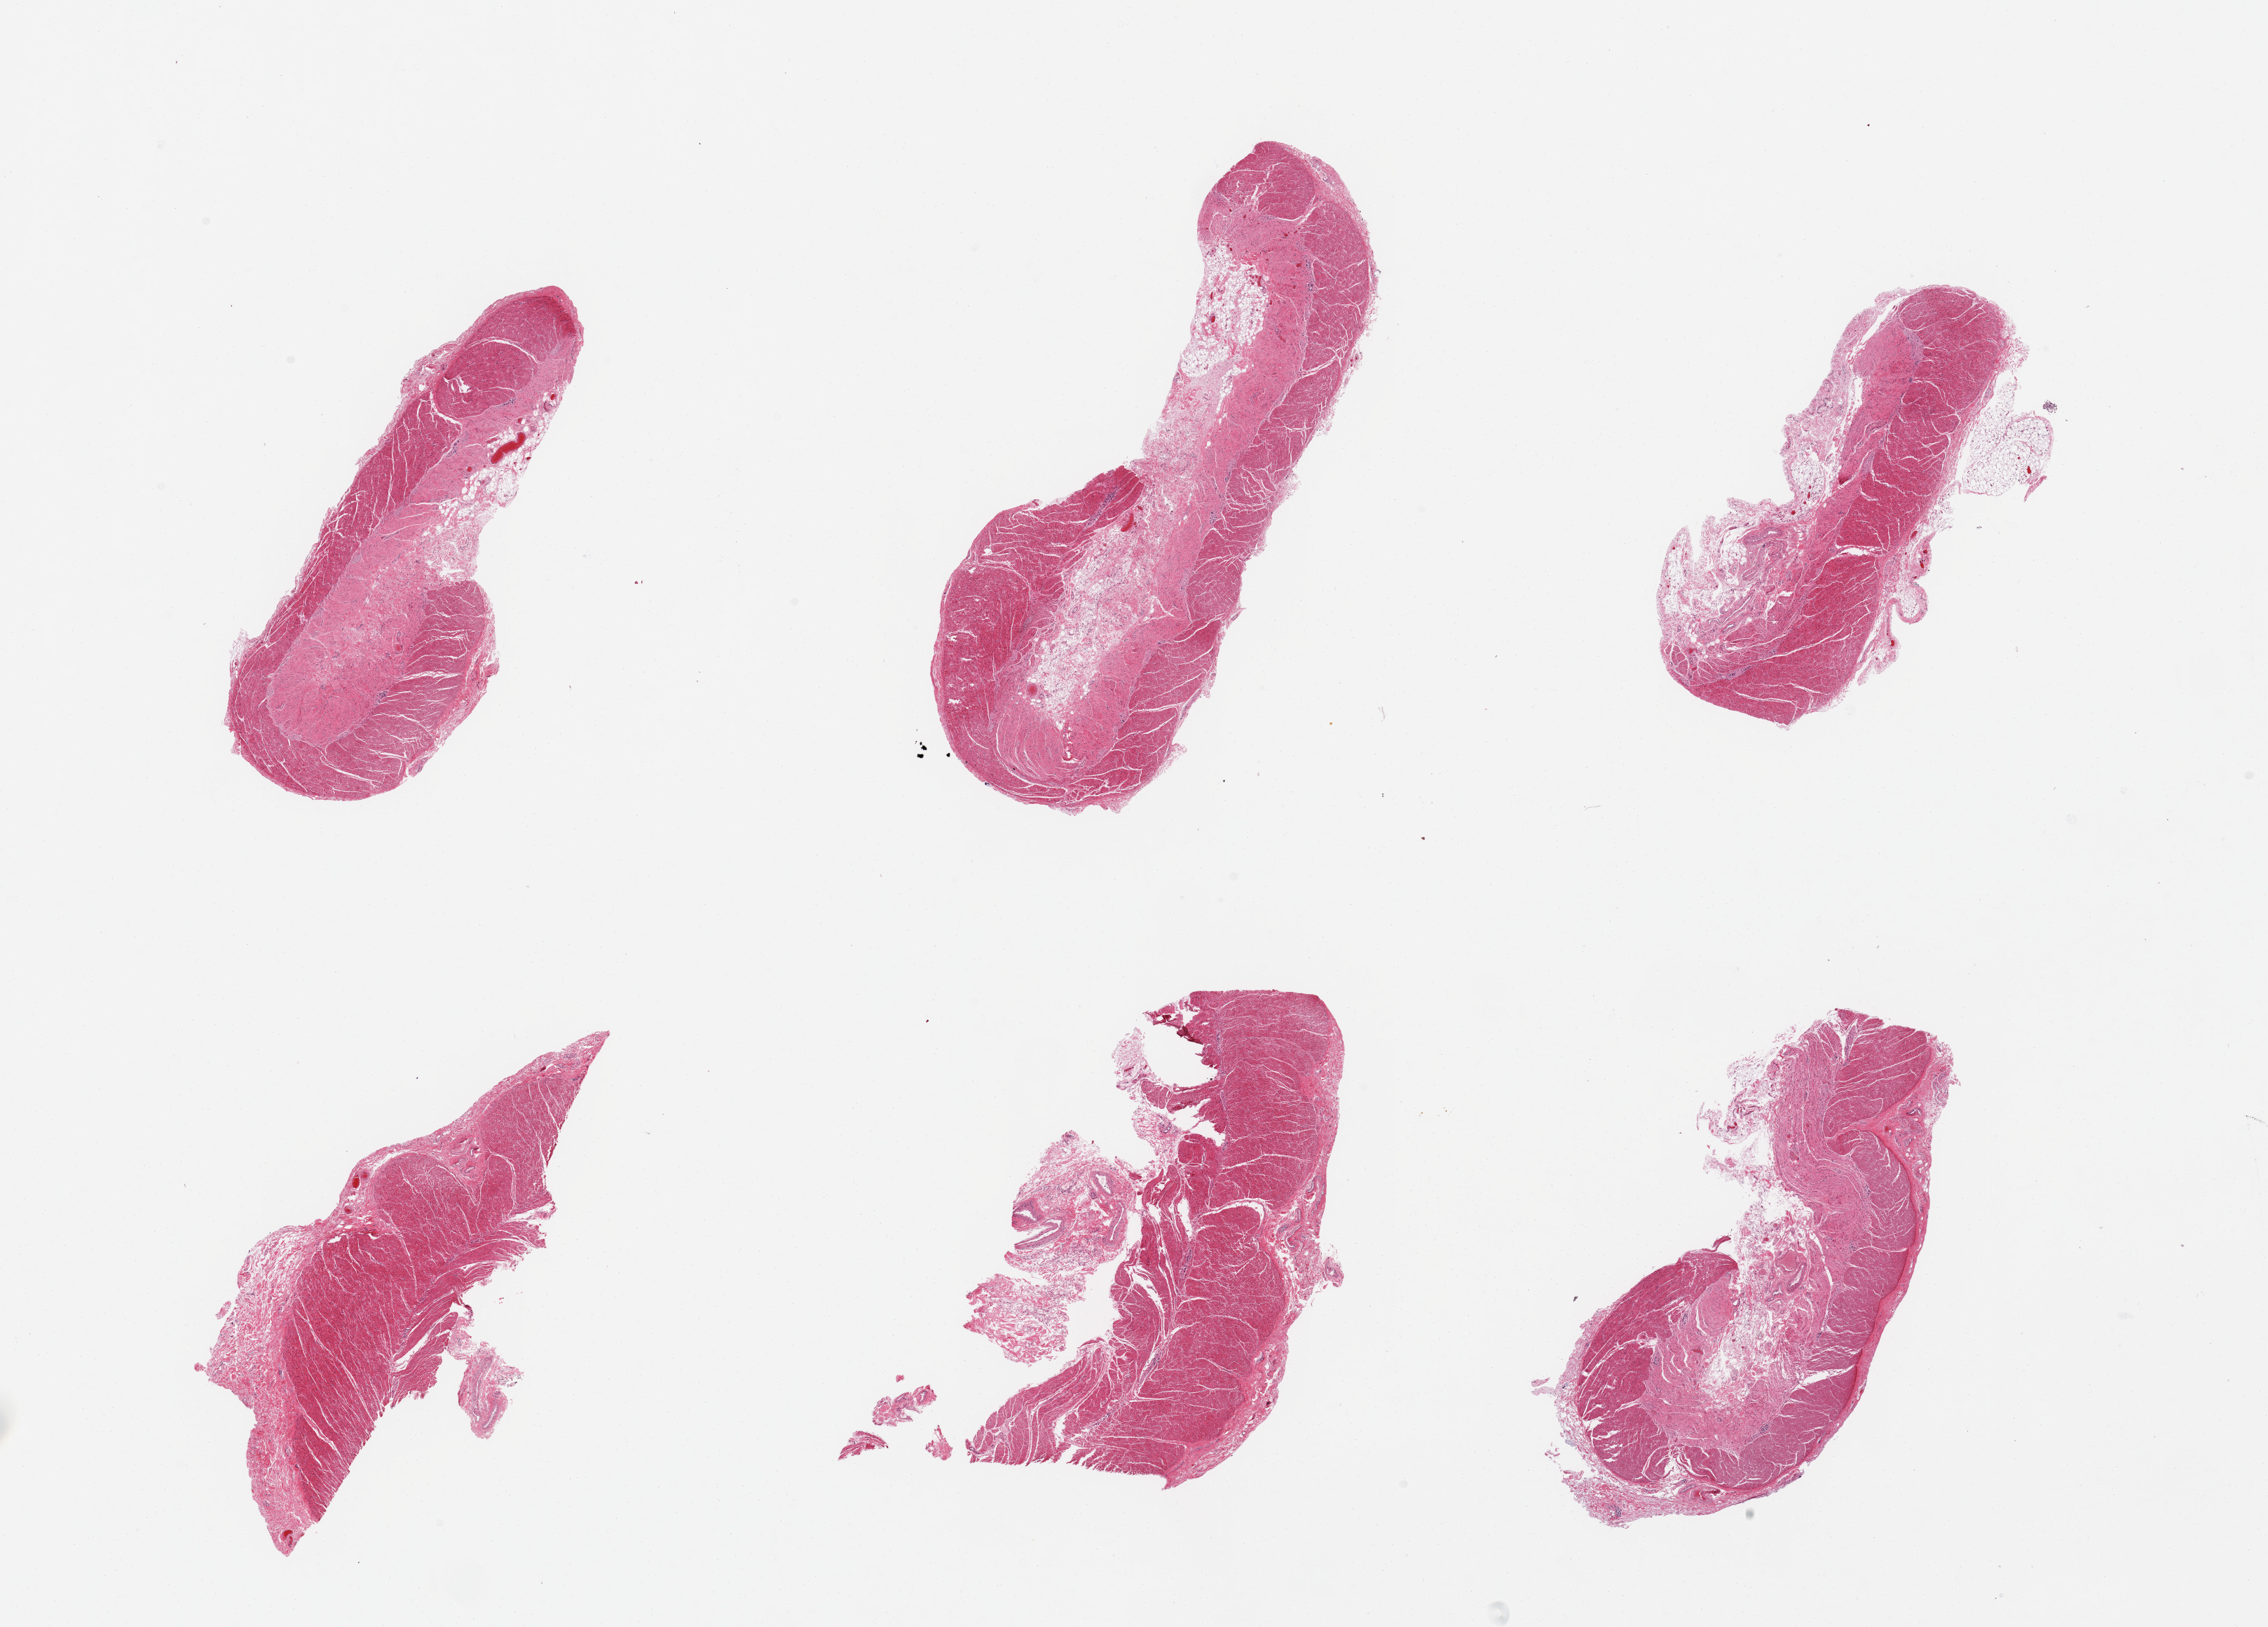
Whole-slide image, haematoxylin and eosin stain, low-resolution overview of the scanned area, about 25.6 x 18.4 mm (from a 20x scan); PAXgene-fixed paraffin-embedded (PFPE) section; target tissue: sigmoid colon; donor tissue sample. Donor: male.
* review note (as recorded): 6 pieces, confirmed target muscularis